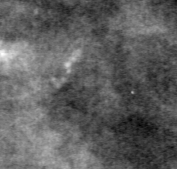
Crop from a digitized film mammogram around one marked abnormality, right breast, MLO view.
- Calcifications, morphology pleomorphic, distribution clustered; BI-RADS assessment category 4; pathology (as recorded): benign.